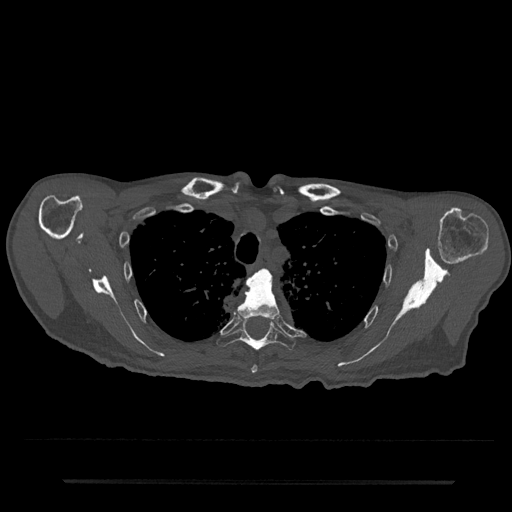
CT including the spine, one axial slice; position 599 of 797 along the scan axis; 120 kVp; bone window (W 1800 / L 400 HU); 512 × 512 image matrix, field of view 427 × 427 mm. Patient: male, 74 years. Case-level facts recorded for this patient, not image findings: primary cancer: prostate.
Structures marked on this image (semi-automatically segmented with operator editing):
- T3 vertebra: bounding box [x1, y1, x2, y2] px = [265, 270, 270, 275]
- T4 vertebra: [237, 270, 280, 374]
- T5 vertebra: [216, 317, 296, 351]